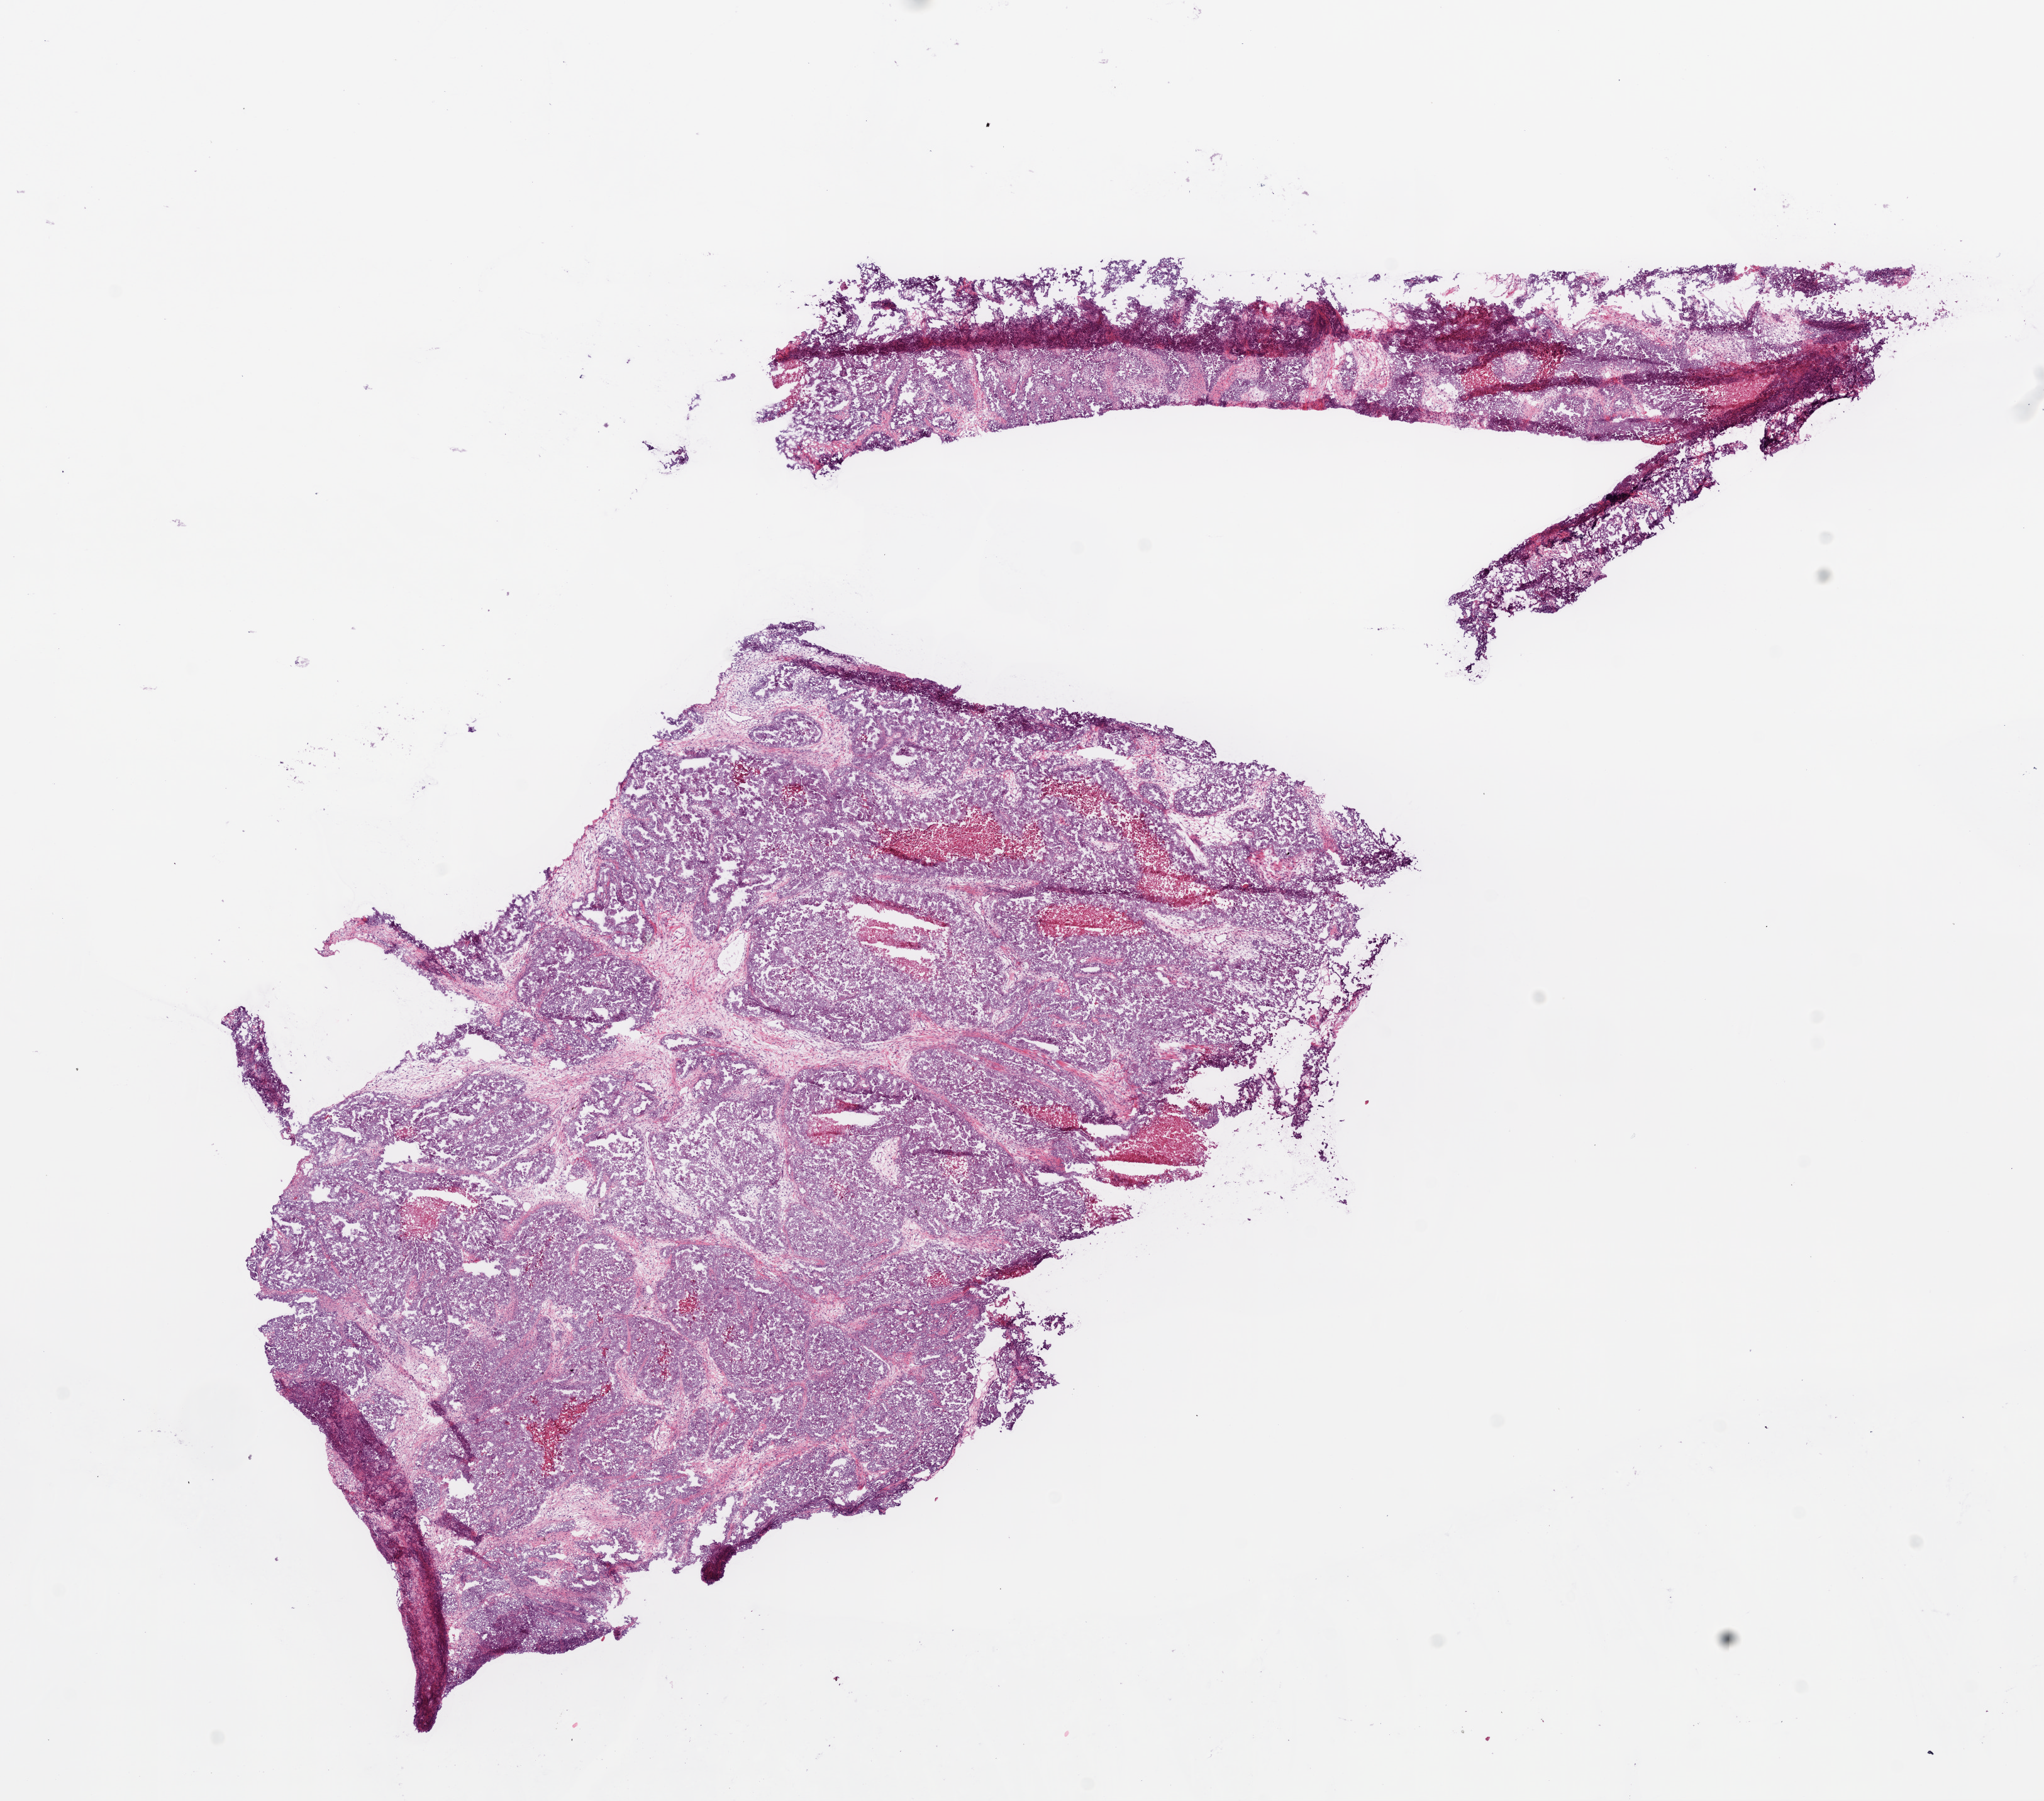
Digitized H&E tissue section (whole slide), whole scanned area (about 13.0 x 11.5 mm) shown as a low-resolution overview, frozen section, sample: primary tumour, ovary. Female patient; age at initial diagnosis 74 years. Histologic grade: G3 (poorly differentiated). Composition of this section per pathologist review: tumour cells 80%, tumour nuclei 90%, normal cells 0%, stromal cells 20%, necrosis 0%.
FIGO stage: IIIC. Histologic diagnosis: Serous cystadenocarcinoma, NOS.